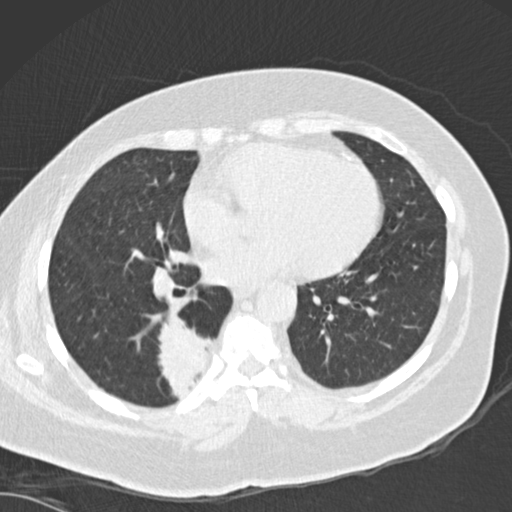
Low-dose screening chest CT, one axial slice. Position 68 of 162 along the scan axis. 120 kVp. Lung window (W 1500 / L -600 HU). 2 mm slice thickness. 512 × 512 image matrix.
Structures marked on this image (outlined manually by an expert reader):
- lesion 1 (tumor, lower lobe of right lung): bounding box (x1, y1, x2, y2) in pixels: (158, 313, 214, 398)